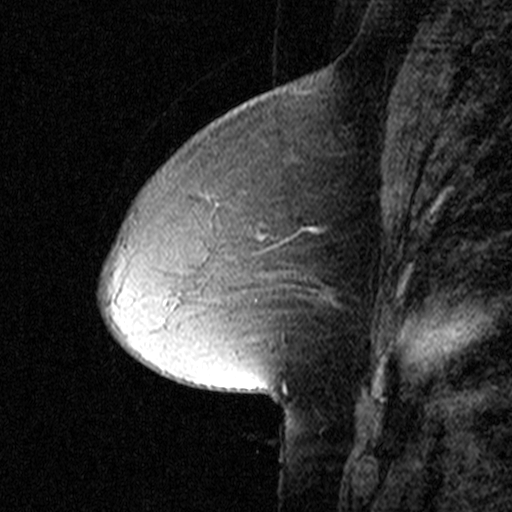
Breast MRI (dynamic contrast-enhanced), one sagittal slice; dynamic contrast-enhanced study with each time point stored as its own series, time point 2 of 3 at this slice position (early post-contrast, ordered by acquisition time); 1.5 T; TE 4.5 ms, TR 11 ms; 3 mm slice thickness; 512 × 512 image matrix. Patient: female, 50 years. Case-level facts recorded for this patient, not image findings: setting: breast cancer imaged before/during neoadjuvant chemotherapy; receptor status: HR-positive, HER2-negative.
Outlined on this slice (semi-automatically segmented with operator editing):
- analysis volume of interest (the breast-tissue region the enhancement analysis was run in; not a lesion): bounding box (x1, y1, x2, y2) in pixels: (154, 164, 313, 287)
- tumour enhancement mask (voxels above the 90 % enhancement threshold inside the analysis volume of interest): (301, 227, 309, 229)